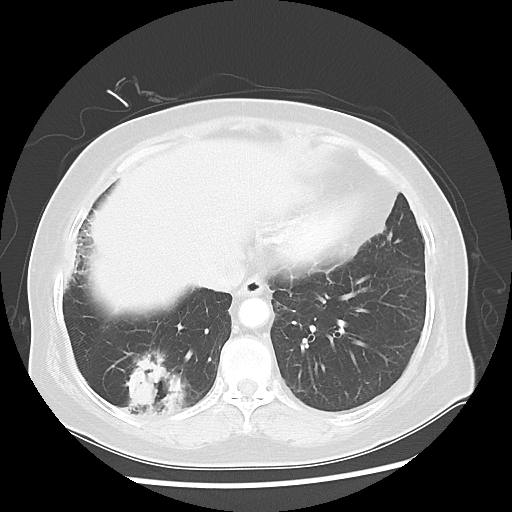
Chest CT, one axial slice. Position 16 of 56 along the scan axis. Lung window (W 1500 / L -600 HU). 5 mm slice thickness. 512 × 512 image matrix, field of view 360 × 360 mm. Patient: female, 64 years. From the clinical record (not read from this slice): clinical TNM (as recorded): Tis N0 M0.
Structures marked on this image (rectangle marked by the reading radiologist):
- lung tumour (recorded histology: adenocarcinoma): box from (x=111, y=345) to (x=201, y=441) px